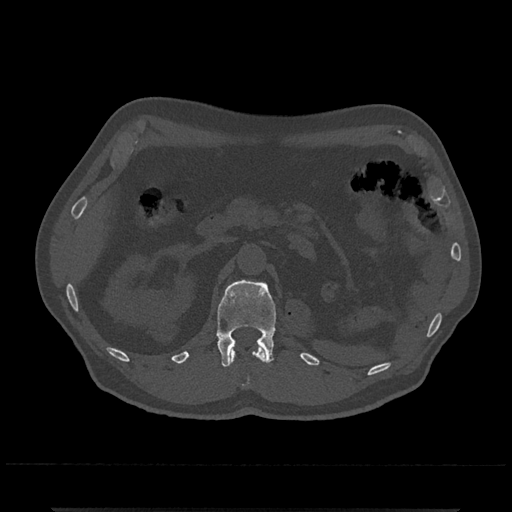
CT including the spine, one axial slice; position 379 of 797 along the scan axis; 120 kVp; bone window (W 1800 / L 400 HU); 0.5 mm slice thickness; 512 × 512 image matrix. Male patient, age 67 years. Case-level facts recorded for this patient, not image findings: primary cancer: prostate.
Structures marked on this image (semi-automatic segmentation, software-assisted and operator-edited):
- L1 vertebra: bounding box <216,279,276,367> (left, top, right, bottom; pixels)
- T12 vertebra: <230,346,266,364>